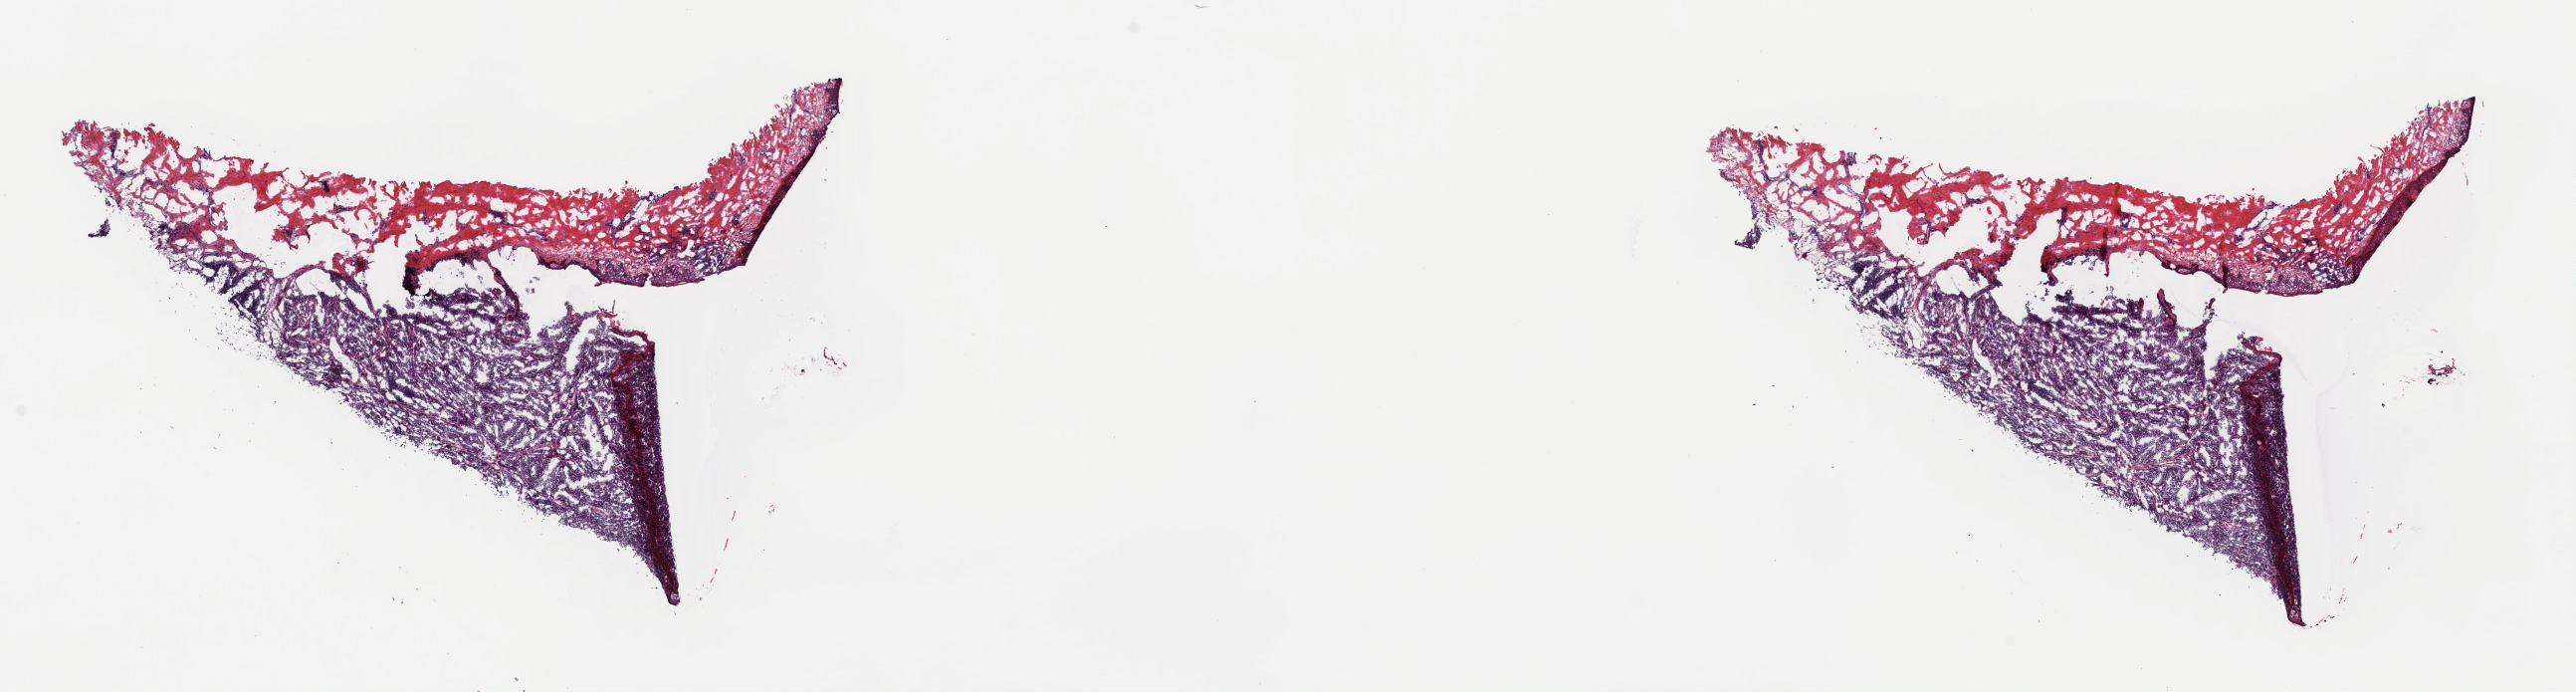
Whole-slide histology image, H&E — whole scanned area (about 20.4 x 5.5 mm, acquisition: 40x scan) shown as a low-resolution overview; frozen section; sample: primary tumour, skin. Female, age 48 years at initial diagnosis. Composition of this section per pathologist review: tumour cells 60%, tumour nuclei 75%, normal cells 40%, stromal cells 0%, necrosis 0%. Infiltration values recorded for this section: lymphocyte infiltration 2%, monocyte infiltration 0%, neutrophil infiltration 0%.
• AJCC pathologic stage: IIC (7th edition)
• diagnosis: Malignant melanoma, NOS